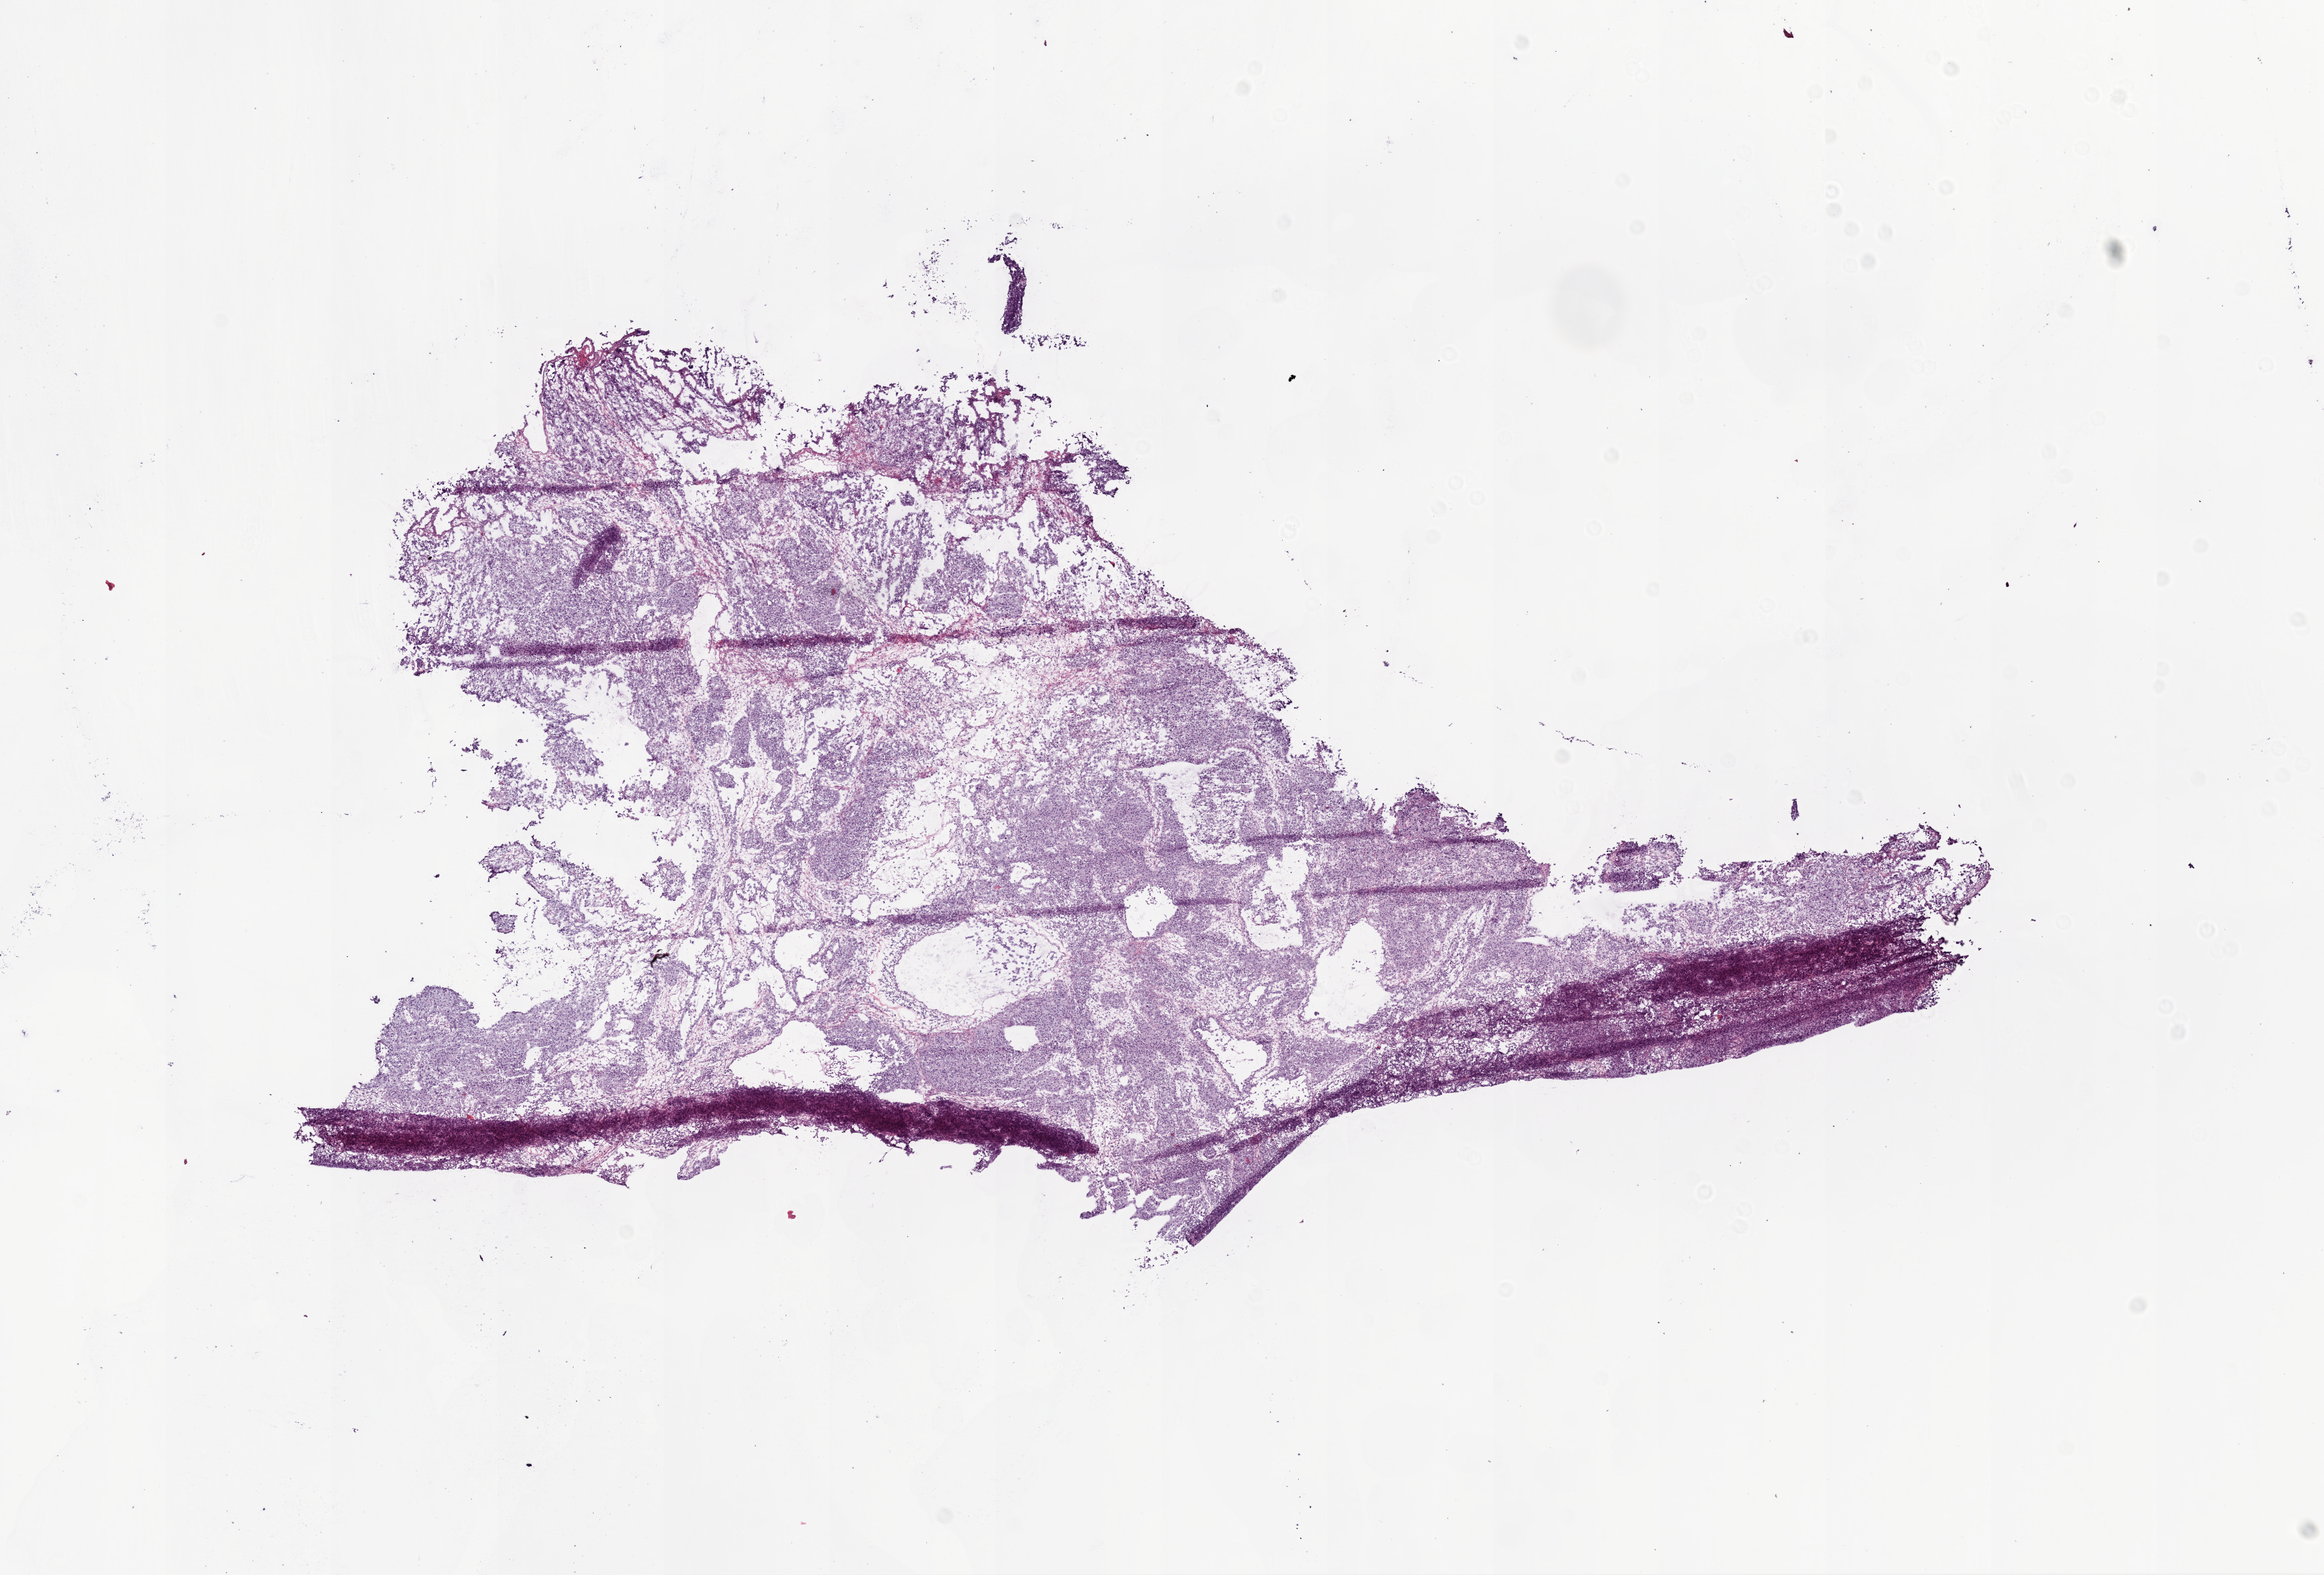
H&E-stained whole-slide image, shown as a low-resolution overview of the whole scanned area (about 14.0 x 9.5 mm, from a 20x scan), frozen section, sample: primary tumour, ovary. Patient: female, age at initial diagnosis 60 years. Histologic grade: G3 (poorly differentiated). Composition of this section per pathologist review: tumour cells 80%, tumour nuclei 98%, normal cells 0%, stromal cells 15%, necrosis 5%.
- FIGO stage: IIIC
- pathologic diagnosis: Serous cystadenocarcinoma, NOS
- laterality: bilateral